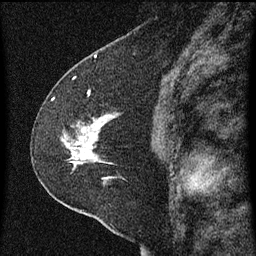
Breast MRI (dynamic contrast-enhanced), one sagittal slice. Slice 36 of 60 in the series (ordered by position). Dynamic contrast-enhanced series, image 2 of 3 at this slice position (ordered by acquisition). 1.5 T. TE 4.2 ms, TR 8 ms. 2 mm slice thickness. 256 × 256 image matrix, field of view 180 × 180 mm. Female patient, age 47 years.
Structures marked on this image (semi-automatically segmented with operator editing):
- analysis volume of interest (the breast-tissue region the enhancement analysis was run in; not a lesion): bounding box (x1, y1, x2, y2) in pixels: (36, 96, 127, 213)
- tumour enhancement mask (voxels above the 70 % enhancement threshold inside the analysis volume of interest): (66, 116, 109, 179)